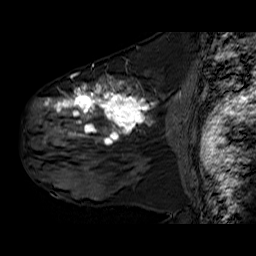
Breast MRI (dynamic contrast-enhanced), one sagittal slice. Position 37 of 60 along the scan axis. Dynamic contrast-enhanced series, time point 2 of 6 at this slice position (early post-contrast). 1.5 T. TE 6.3 ms, TR 32.9 ms. 4 mm slice thickness. 256 × 256 image matrix, field of view 200 × 200 mm. Female patient. Case-level facts recorded for this patient, not image findings: setting: breast cancer imaged before/during neoadjuvant chemotherapy; receptor status: HER2-positive.
Structures marked on this image (semi-automatically segmented with operator editing):
- analysis volume of interest (the breast-tissue region the enhancement analysis was run in; not a lesion): bounding box <30,78,176,180> (left, top, right, bottom; pixels)
- tumour enhancement mask (voxels above the 100 % enhancement threshold inside the analysis volume of interest): <44,79,158,146>